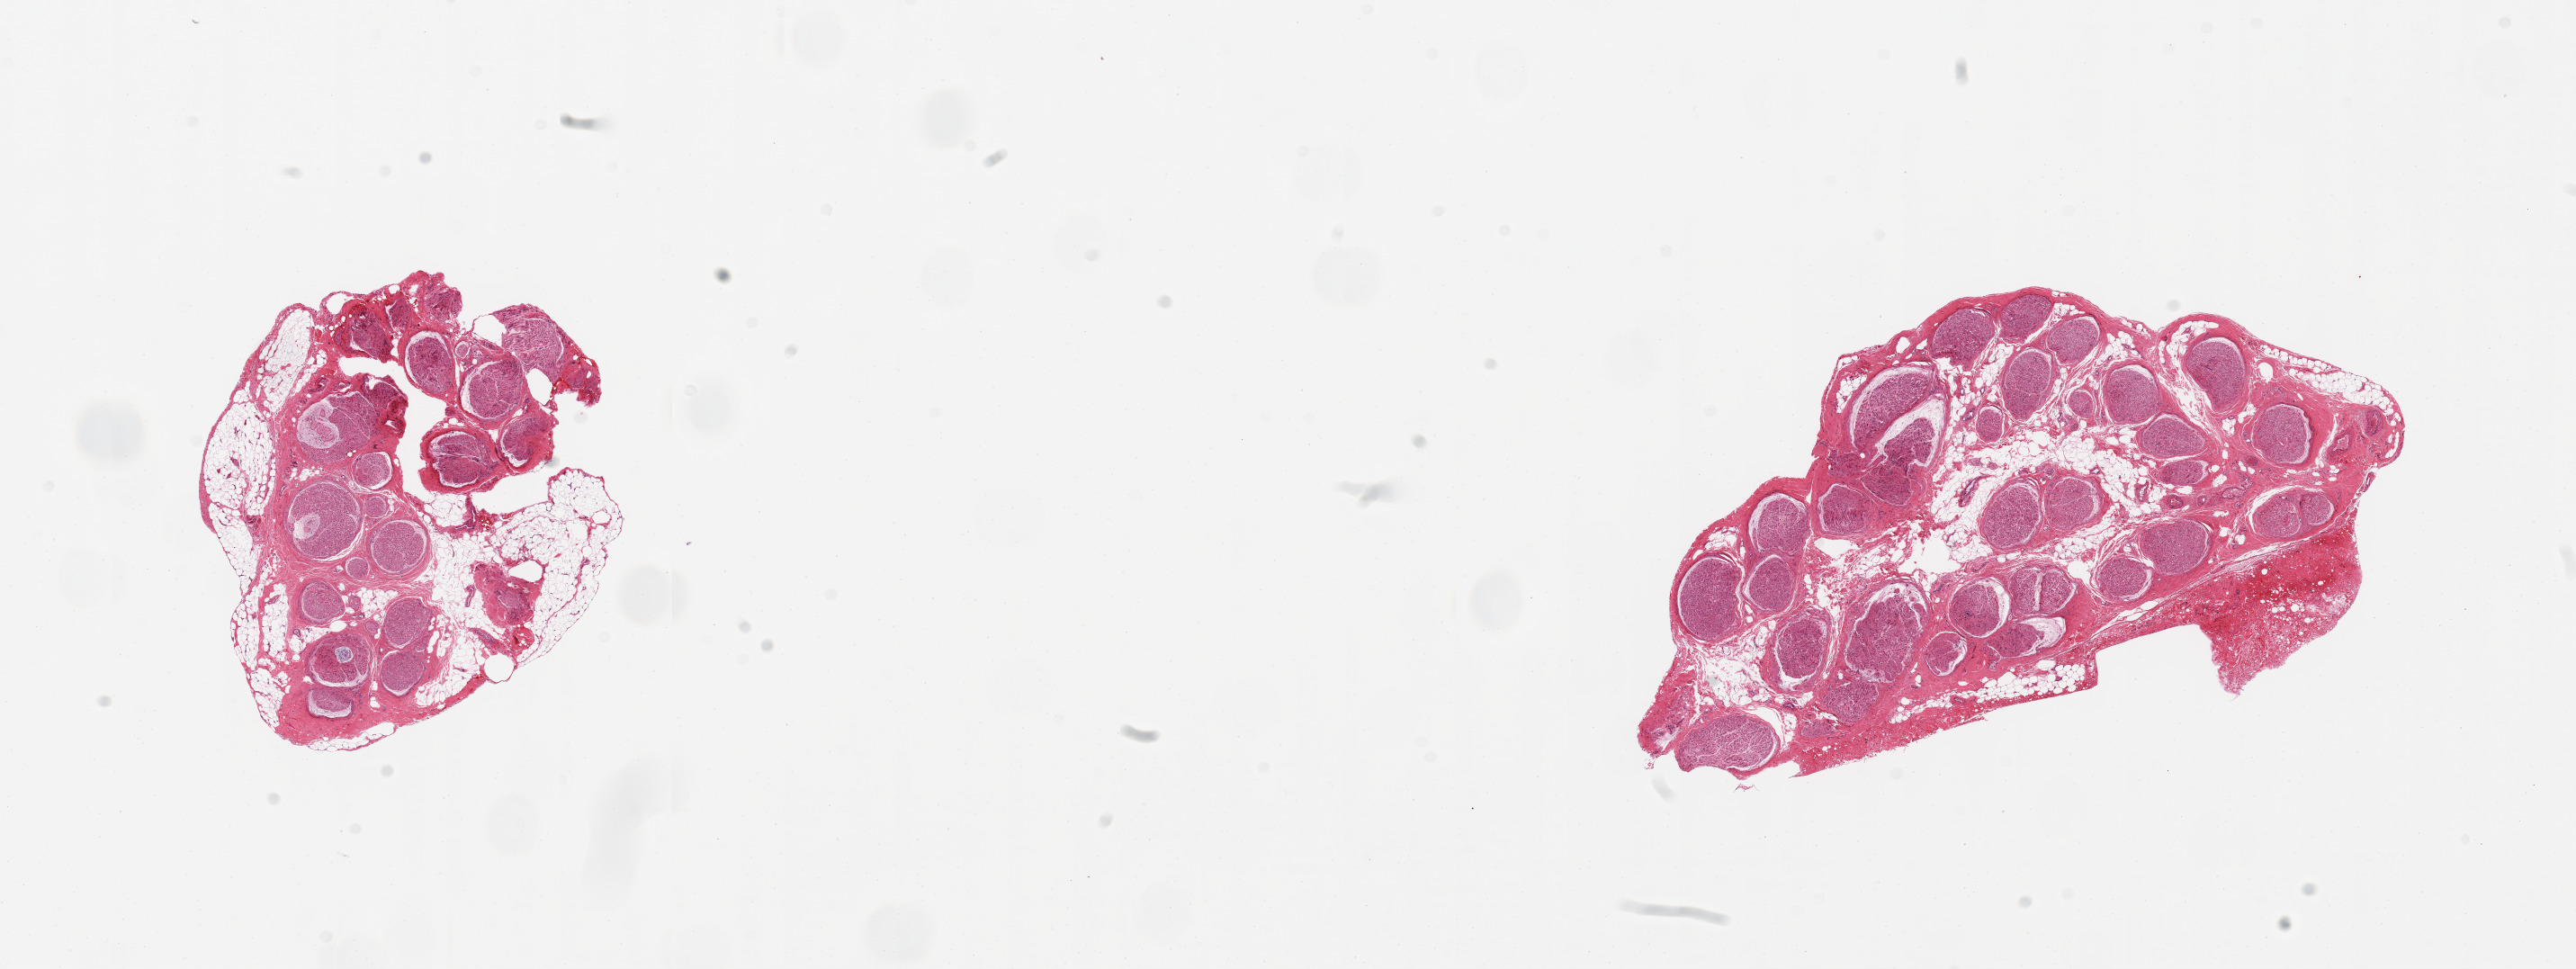
Haematoxylin and eosin whole-slide image, low-resolution overview of the scanned area, about 22.6 x 8.5 mm (from a 20x scan). PAXgene-fixed, paraffin-embedded tissue. Sampled site (target tissue): tibial nerve. Tissue donor sample.
* pathologist's review note for this sample: 2 pieces; up to 40% fat in and around nerve bundles